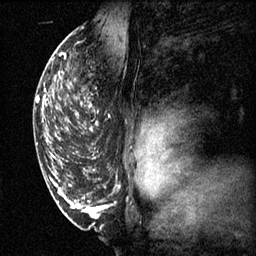
Breast MRI (dynamic contrast-enhanced), one sagittal slice. Slice 39 of 60 in the series (ordered by position). 3 images stored at this slice position (order not interpretable as contrast timing). 1.5 T. TE 4.2 ms, TR 11.1 ms. 256 × 256 image matrix, field of view 180 × 180 mm. Patient: female, 50 years.
Structures marked on this image (semi-automatically segmented with operator editing):
- analysis volume of interest (the breast-tissue region the enhancement analysis was run in; not a lesion): bounding box [x1, y1, x2, y2] px = [68, 68, 103, 139]
- tumour enhancement mask (voxels above the 70 % enhancement threshold inside the analysis volume of interest): [68, 96, 99, 131]